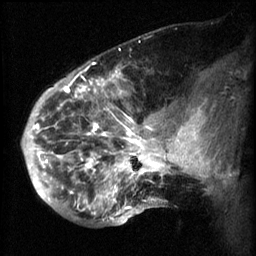
Breast MRI (dynamic contrast-enhanced), one sagittal slice; slice 21 of 60 in the series (ordered by position); 3 images stored at this slice position (order not interpretable as contrast timing); 1.5 T; TE 4.2 ms, TR 8.2 ms; 256 × 256 image matrix. Patient: female, 50 years.
Annotated regions visible in this slice (semi-automatic segmentation, software-assisted and operator-edited):
- analysis volume of interest (the breast-tissue region the enhancement analysis was run in; not a lesion): box from (x=50, y=64) to (x=169, y=217) px
- tumour enhancement mask (voxels above the 70 % enhancement threshold inside the analysis volume of interest): (x=50, y=64)–(x=169, y=215)